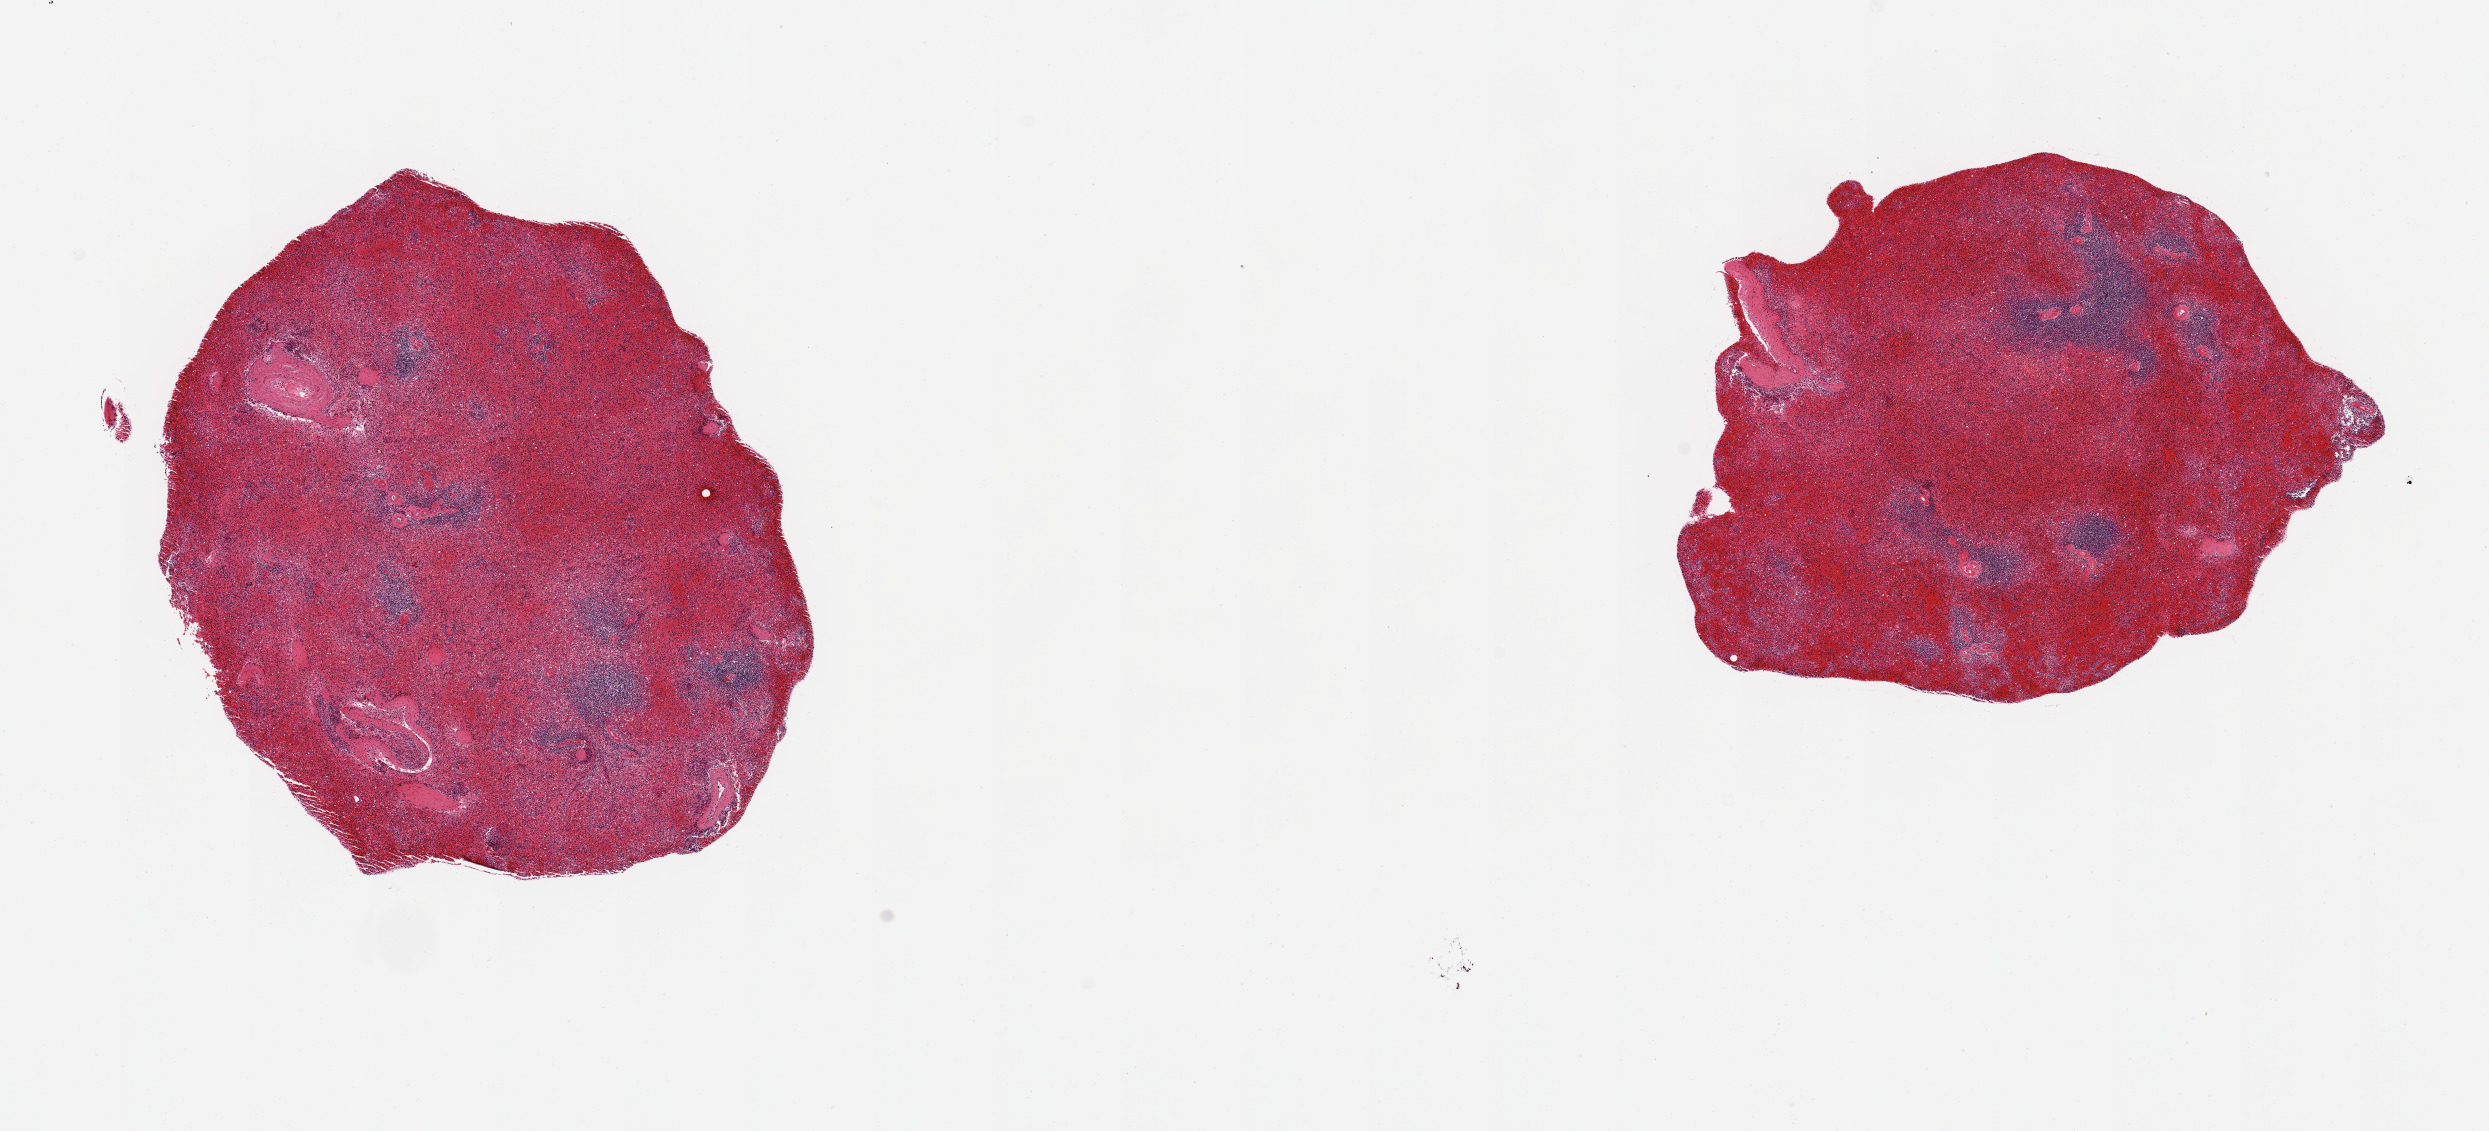
Whole-slide image, haematoxylin and eosin stain, brightfield, low-resolution overview of the scanned area, about 19.7 x 8.9 mm. PAXgene-fixed paraffin-embedded (PFPE) section. Section of spleen (target tissue). Donor tissue sample. Male donor.
Pathologist's review note for this sample: 2 pieces, marked congestion/autolysis.